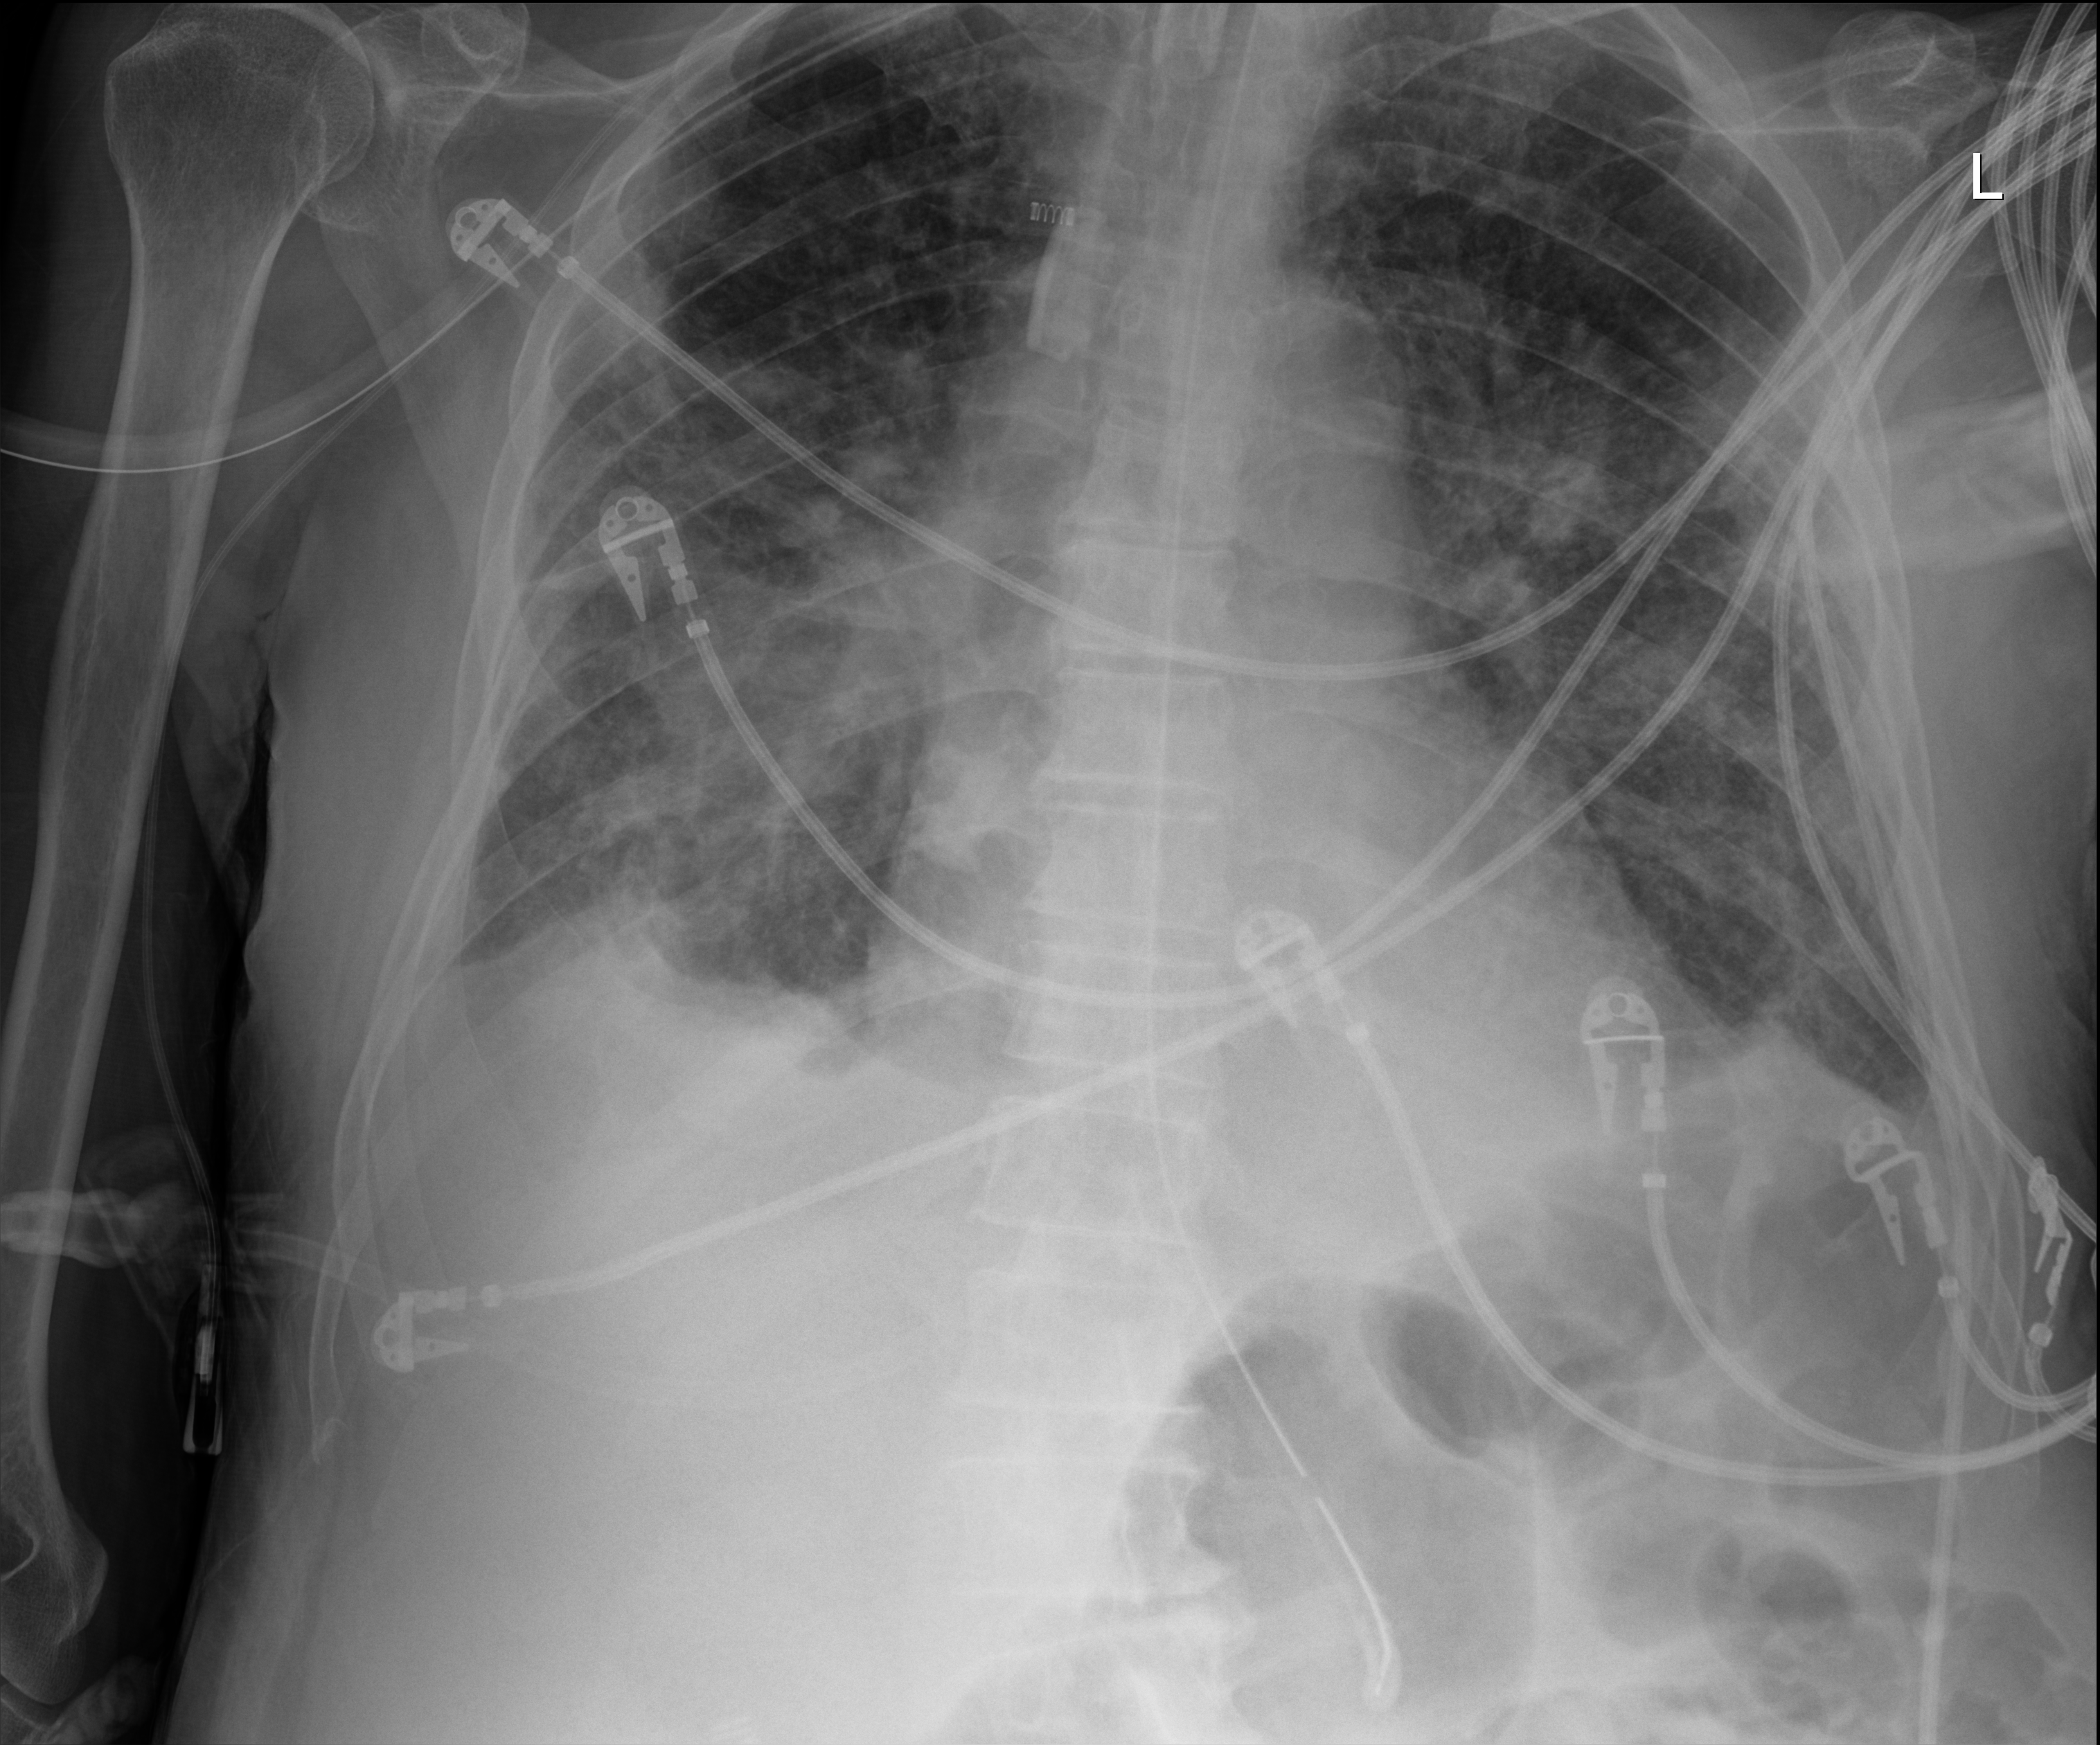
Chest X-ray (portable); anteroposterior (AP) projection. Male patient hospitalised with COVID-19, age 75–90 years.
Admission-level facts for this patient (not findings on this image; timing relative to this image not recorded): admitted to intensive care during this hospital stay: yes; length of hospital stay: 70 days.